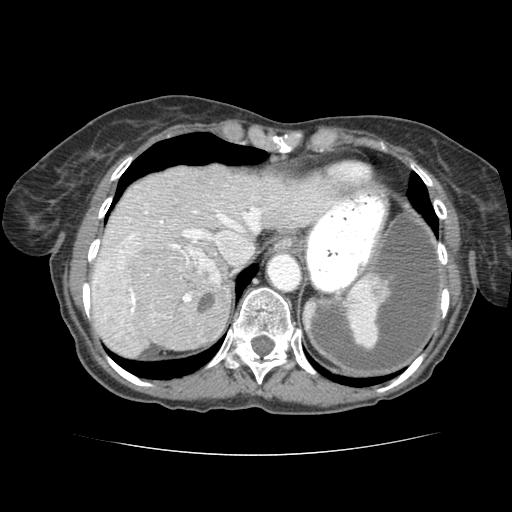
Contrast-enhanced abdominal CT (liver protocol), one axial slice; slice 65 of 77 in the series (ordered by position); reconstruction kernel STANDARD; soft-tissue window (W 400 / L 40 HU); 2.5 mm slice thickness; 512 × 512 image matrix, field of view 340 × 340 mm. From the clinical record (not read from this slice): diagnosis: hepatocellular carcinoma (patient treated with transarterial chemoembolisation; whether this scan precedes or follows treatment is not stated here); TNM stage (as recorded): Stage-I; Child-Pugh class: A; tumour nodularity: uninodular; tumour size: 7.6 cm.
Structures marked on this image (semi-automatically segmented with operator editing):
- abdominal aorta: bounding box (x1, y1, x2, y2) in pixels: (267, 251, 299, 289)
- liver parenchyma outside the tumour (the mass and vessels are separate outlines, so this box may not span the whole liver): (88, 166, 290, 348)
- mass: (129, 245, 225, 343)
- liver vessels: (120, 210, 212, 304)